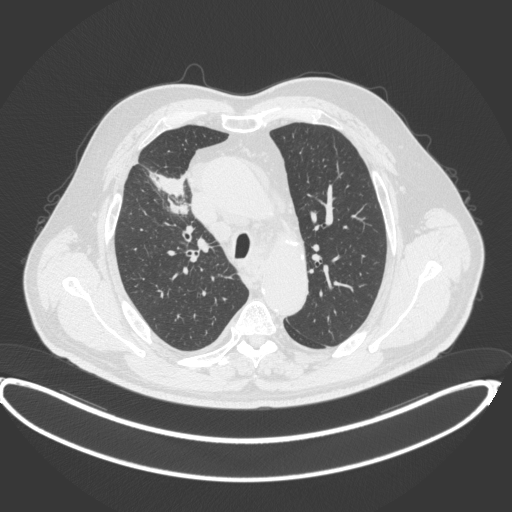
Chest CT, one axial slice; slice 294 of 395 in the series (ordered by position); reconstruction kernel B31f; 120 kVp; lung window (W 1500 / L -600 HU); 1 mm slice thickness; 512 × 512 image matrix, field of view 448 × 448 mm. Patient: male, 62 years. From the clinical record (not read from this slice): clinical TNM (as recorded): T1c N3 M1c.
Outlined on this slice (rectangle marked by the reading radiologist):
- lung tumour (recorded histology: adenocarcinoma): bounding box (x1, y1, x2, y2) in pixels: (148, 170, 189, 217)